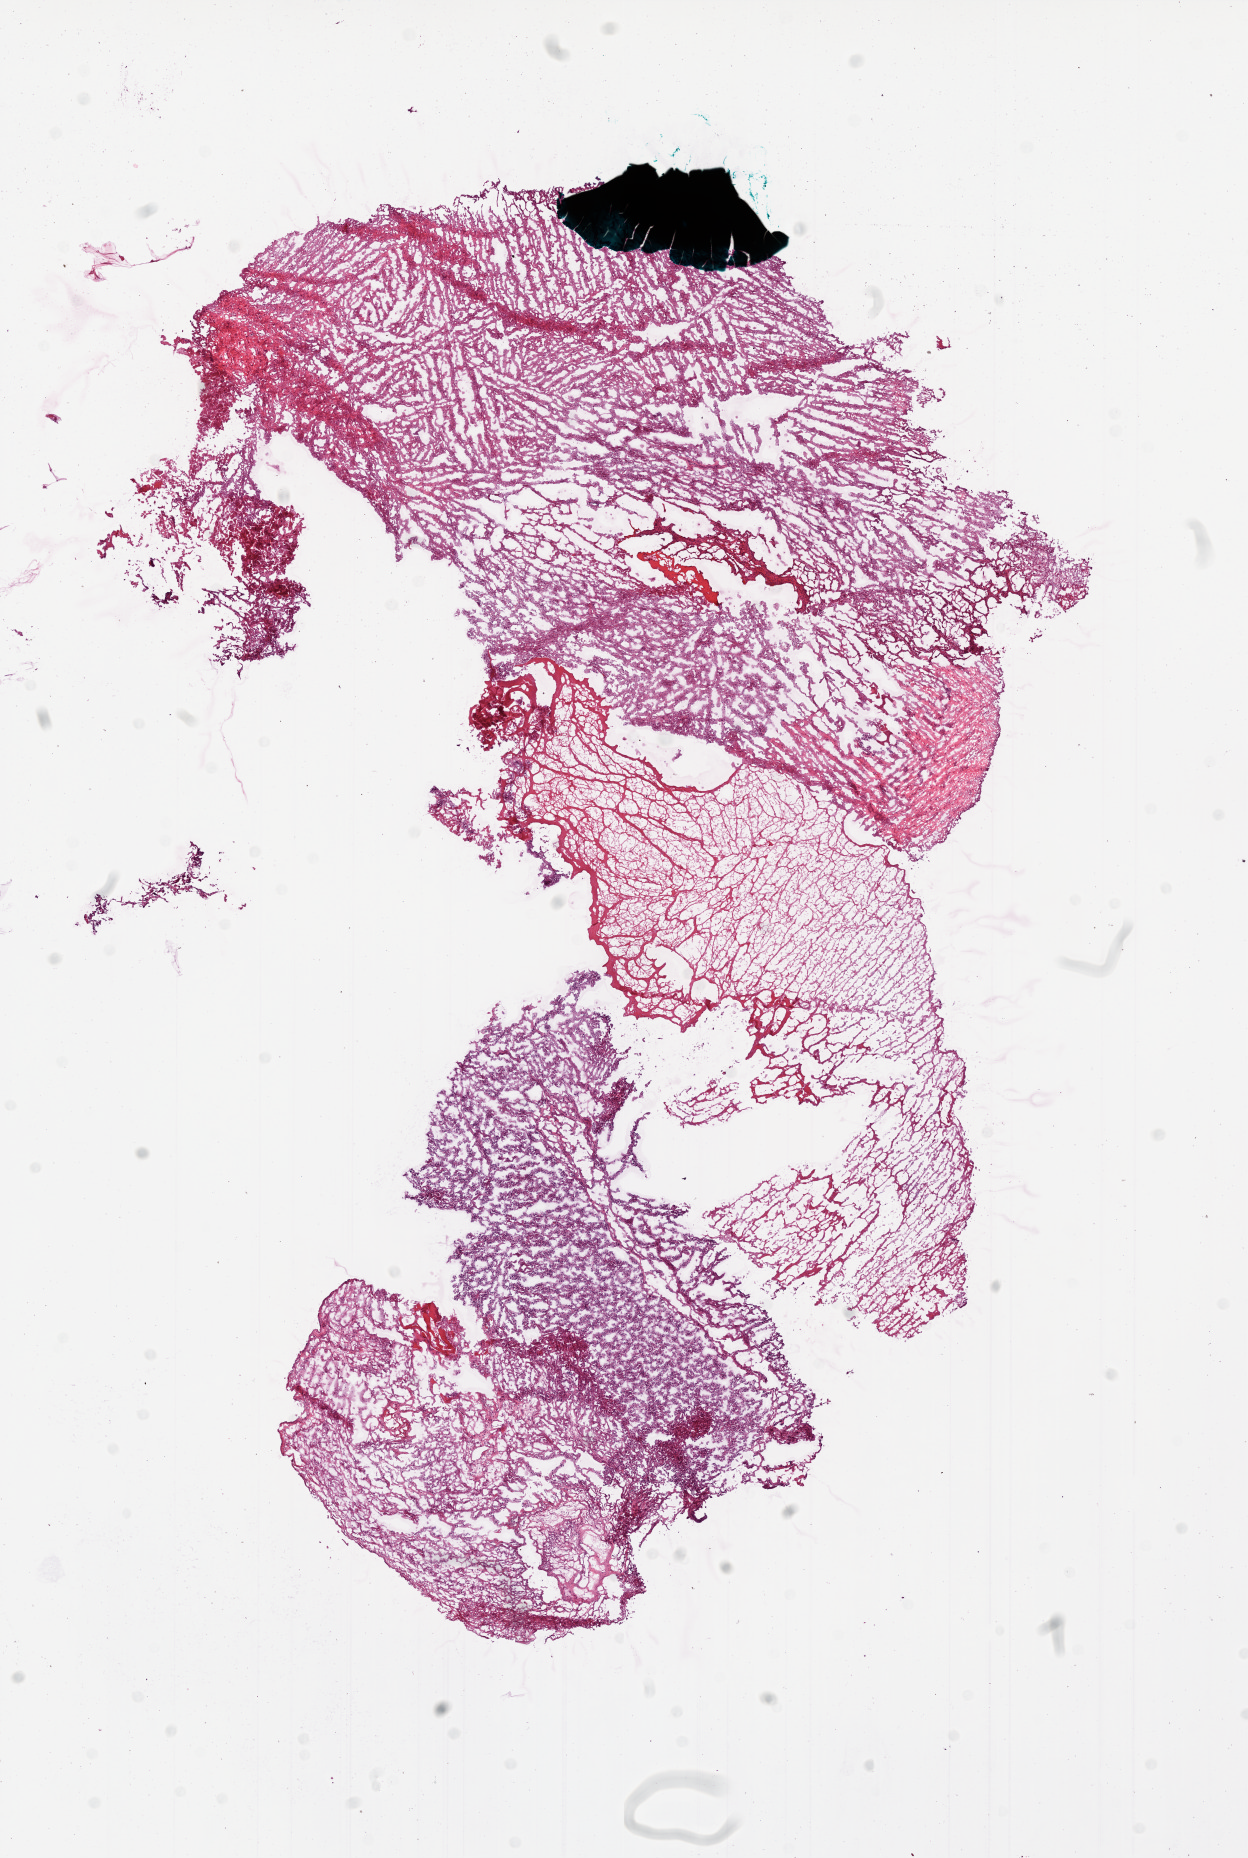
H&E whole-slide image — shown as a low-resolution overview of the whole scanned area (about 10.0 x 14.9 mm); frozen section from the bottom of the tissue portion; sample: primary tumour, brain. Female patient; age at initial diagnosis 46 years. Slide review estimates, as recorded: tumour cells 30%, tumour nuclei 100%, normal cells 20%, stromal cells 20%, necrosis 30%.
* histologic diagnosis: Glioblastoma